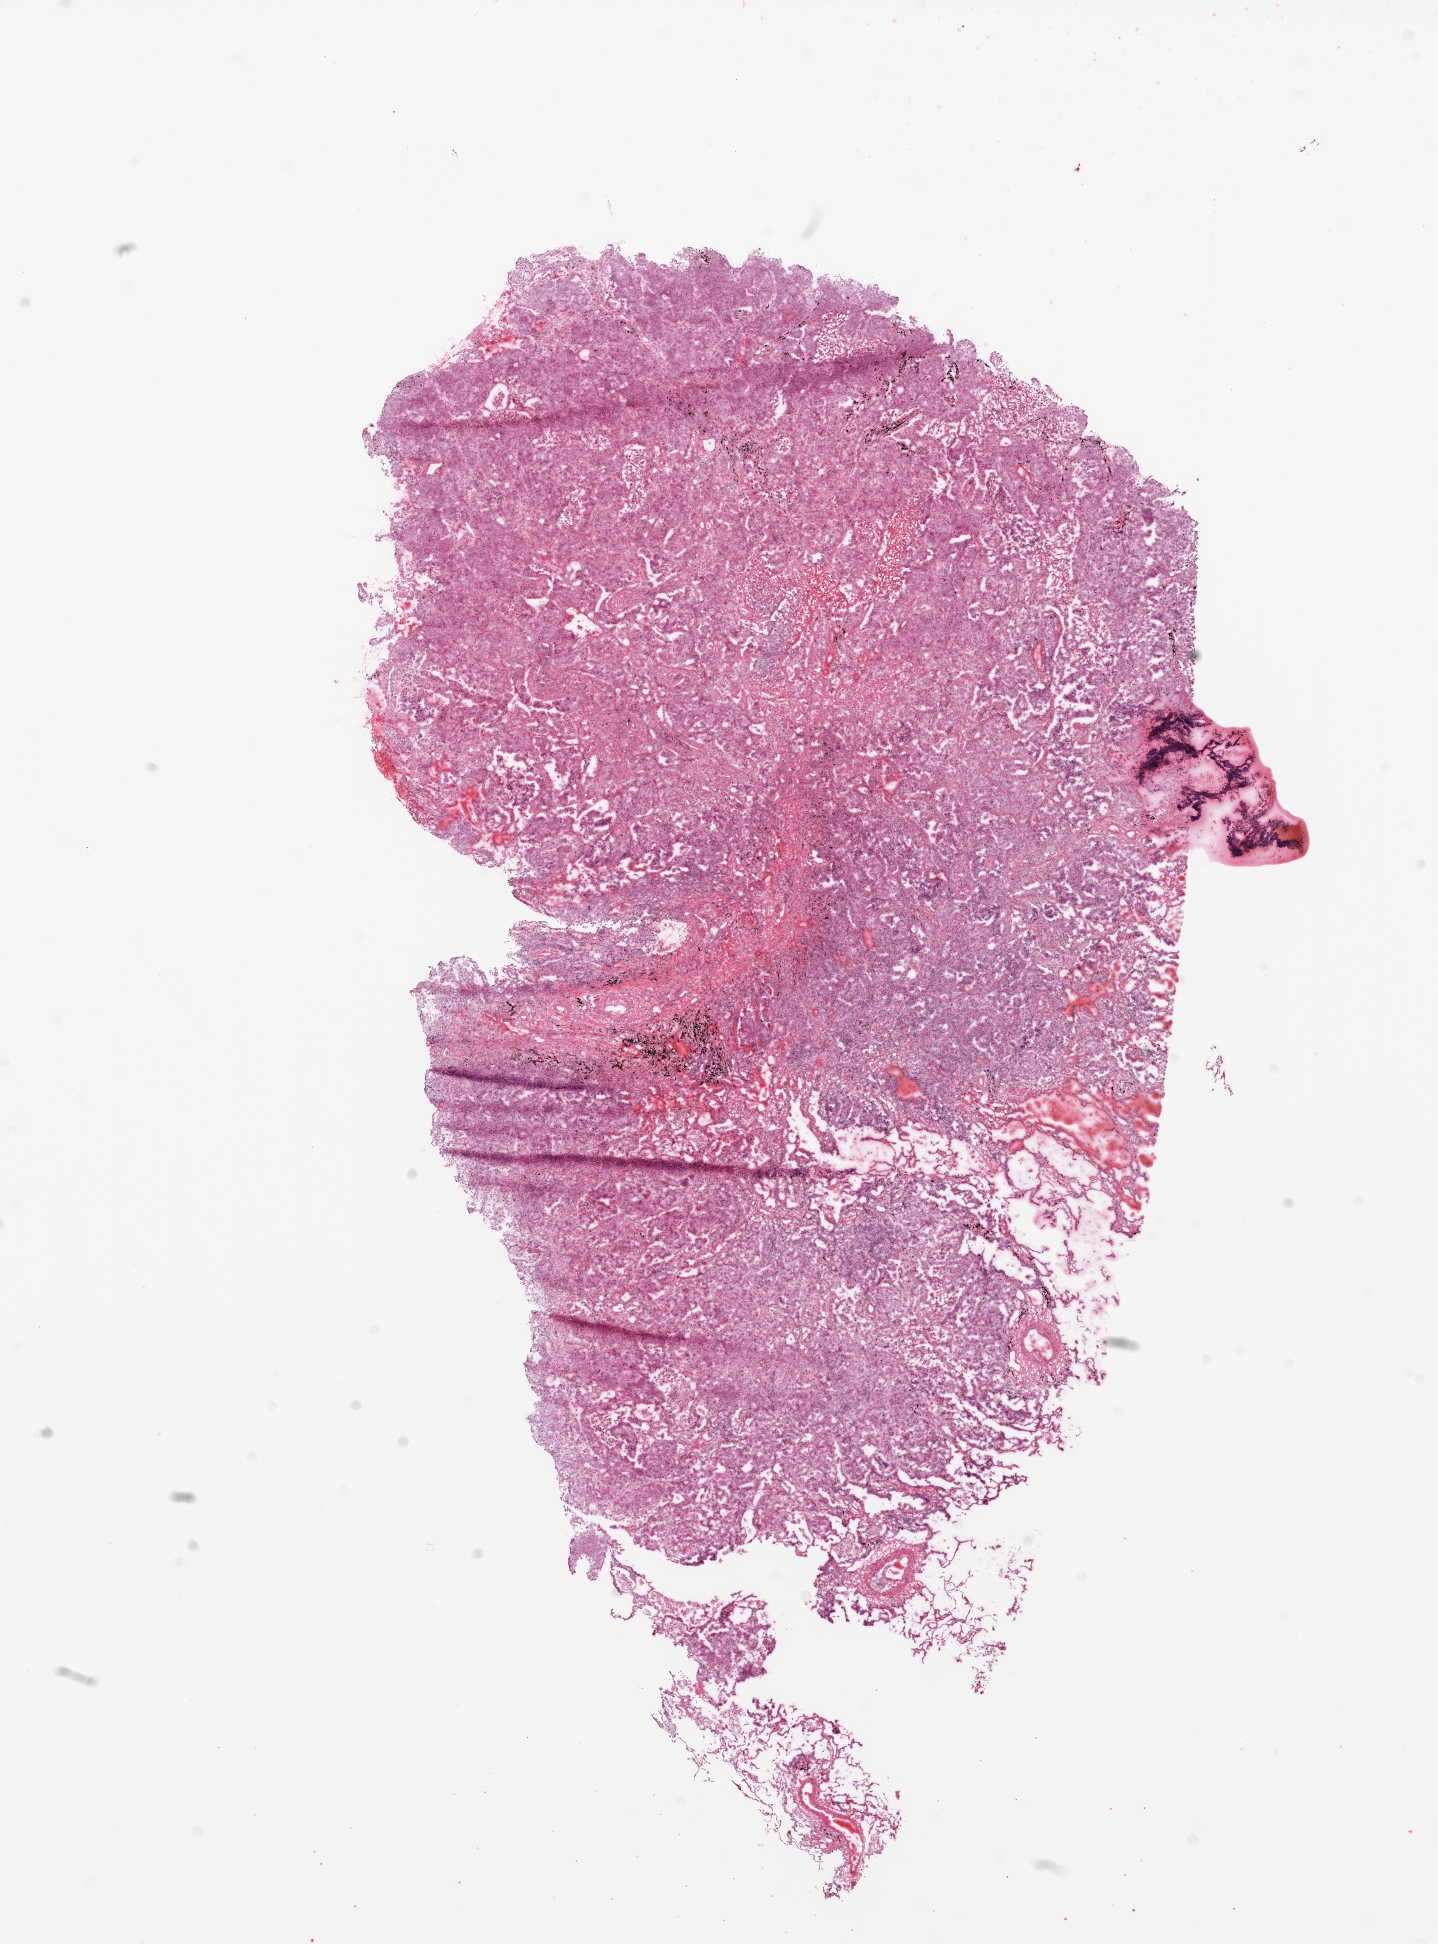
H&E whole-slide image — shown as a low-resolution overview of the whole scanned area (about 11.6 x 15.7 mm), frozen section, lung, primary tumour sample. Male, age 62 years at initial diagnosis. Slide review estimates, as recorded: tumour nuclei 80%, necrosis 5%.
AJCC pathologic stage: IA. Diagnosis: Squamous cell carcinoma, NOS.